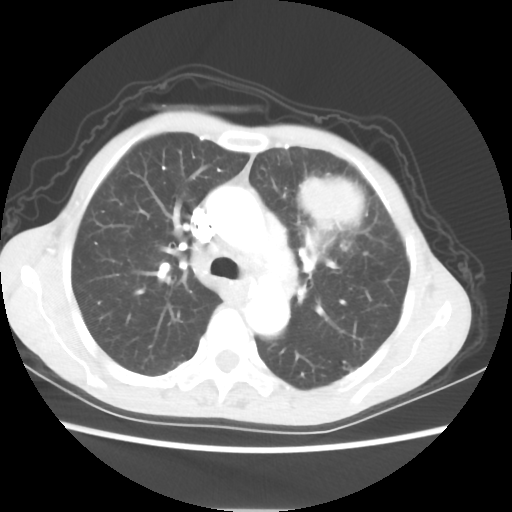
Chest CT, one axial slice. Slice 39 of 56 in the series (ordered by position). Lung window (W 1500 / L -600 HU). 512 × 512 image matrix, field of view 331 × 331 mm. Patient: female, 60 years. Case-level facts recorded for this patient, not image findings: clinical TNM (as recorded): T4 N1 M0.
Structures marked on this image (rectangle marked by the reading radiologist):
- lung tumour (recorded histology: adenocarcinoma): bounding box <293,178,363,230> (left, top, right, bottom; pixels)